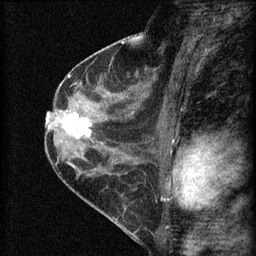
Breast MRI (dynamic contrast-enhanced), one sagittal slice; position 35 of 60 along the scan axis; dynamic contrast-enhanced series, image 2 of 4 at this slice position (ordered by acquisition); 1.5 T; TE 4.2 ms, TR 8.2 ms; 256 × 256 image matrix, field of view 180 × 180 mm. Patient: female, 45 years.
Annotated regions visible in this slice (semi-automatically segmented with operator editing):
- analysis volume of interest (the breast-tissue region the enhancement analysis was run in; not a lesion): bounding box <58,107,98,147> (left, top, right, bottom; pixels)
- tumour enhancement mask (voxels above the 70 % enhancement threshold inside the analysis volume of interest): <63,113,91,138>